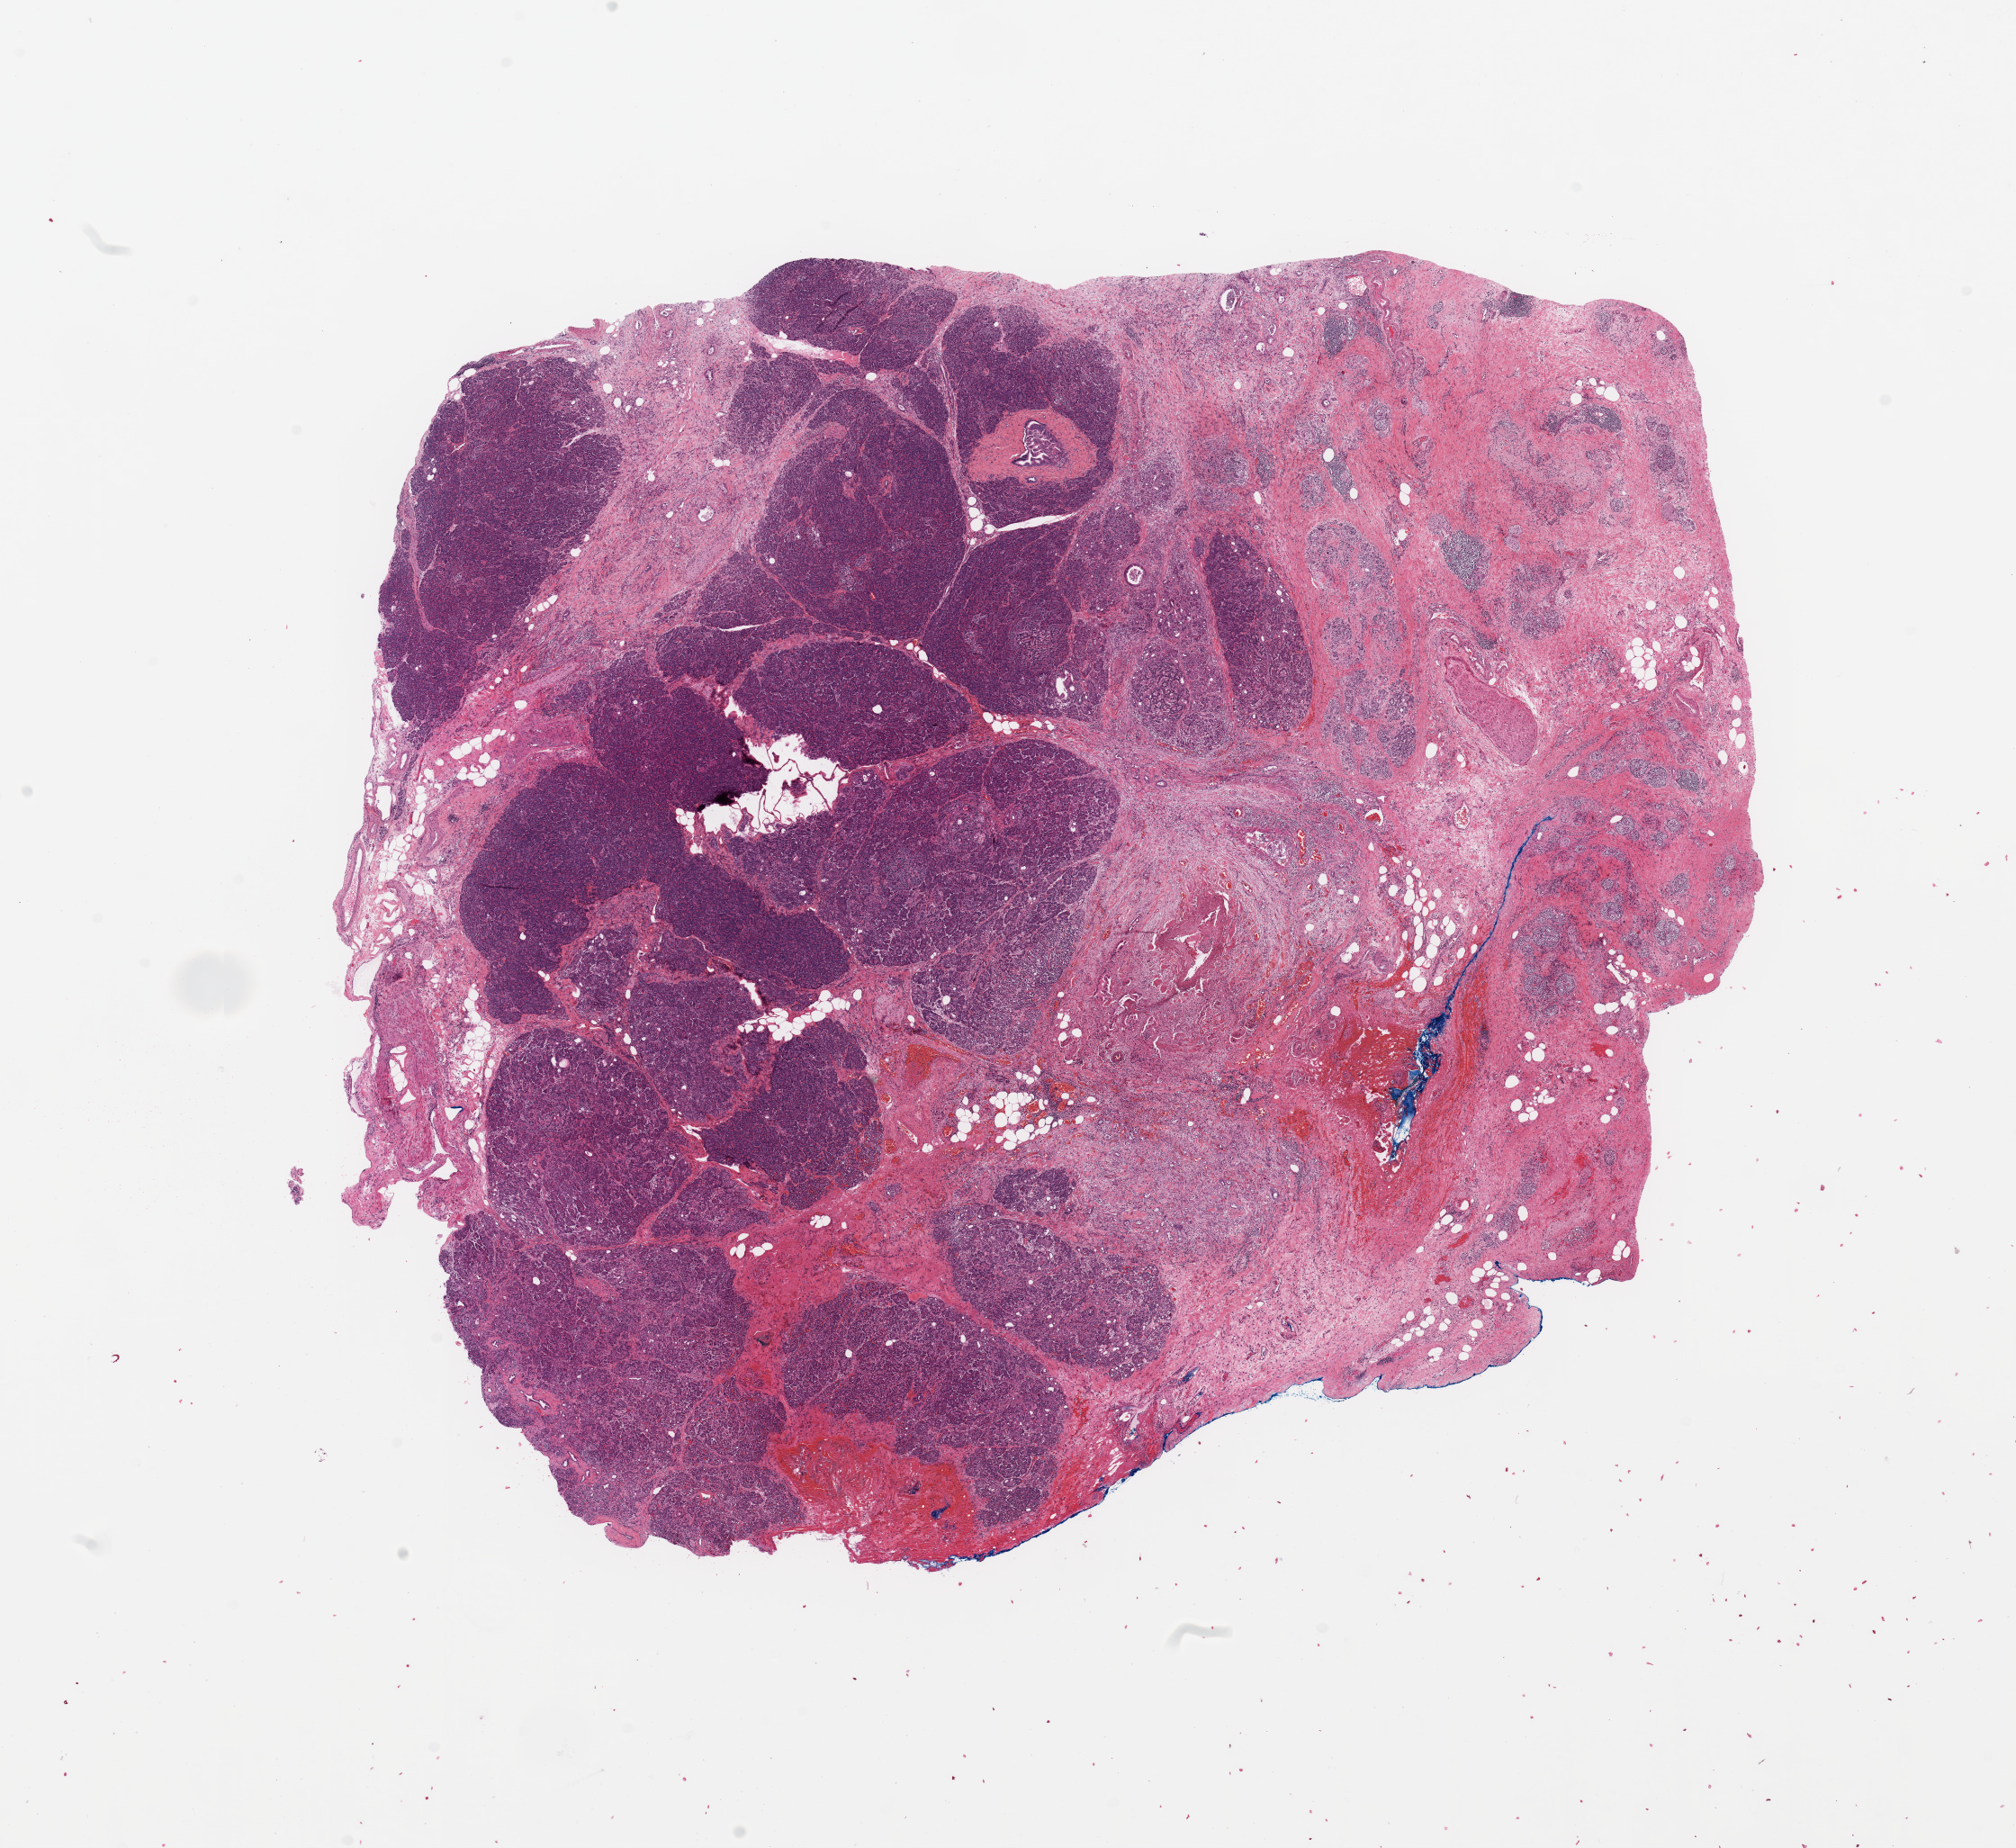
Whole-slide histology image, H&E-stained, low-resolution overview of the scanned area, about 17.7 x 16.2 mm (from a 20x scan), tumour tissue sample, sampled site: pancreas. Female, 64 y/o. Histologic grade: G2 (moderately differentiated). Composition of this section per pathologist review: tumour nuclei 10%, necrosis 0%.
Primary tumour site (as recorded): head. AJCC pathologic stage: IIA. Diagnosis: Infiltrating duct carcinoma, NOS.